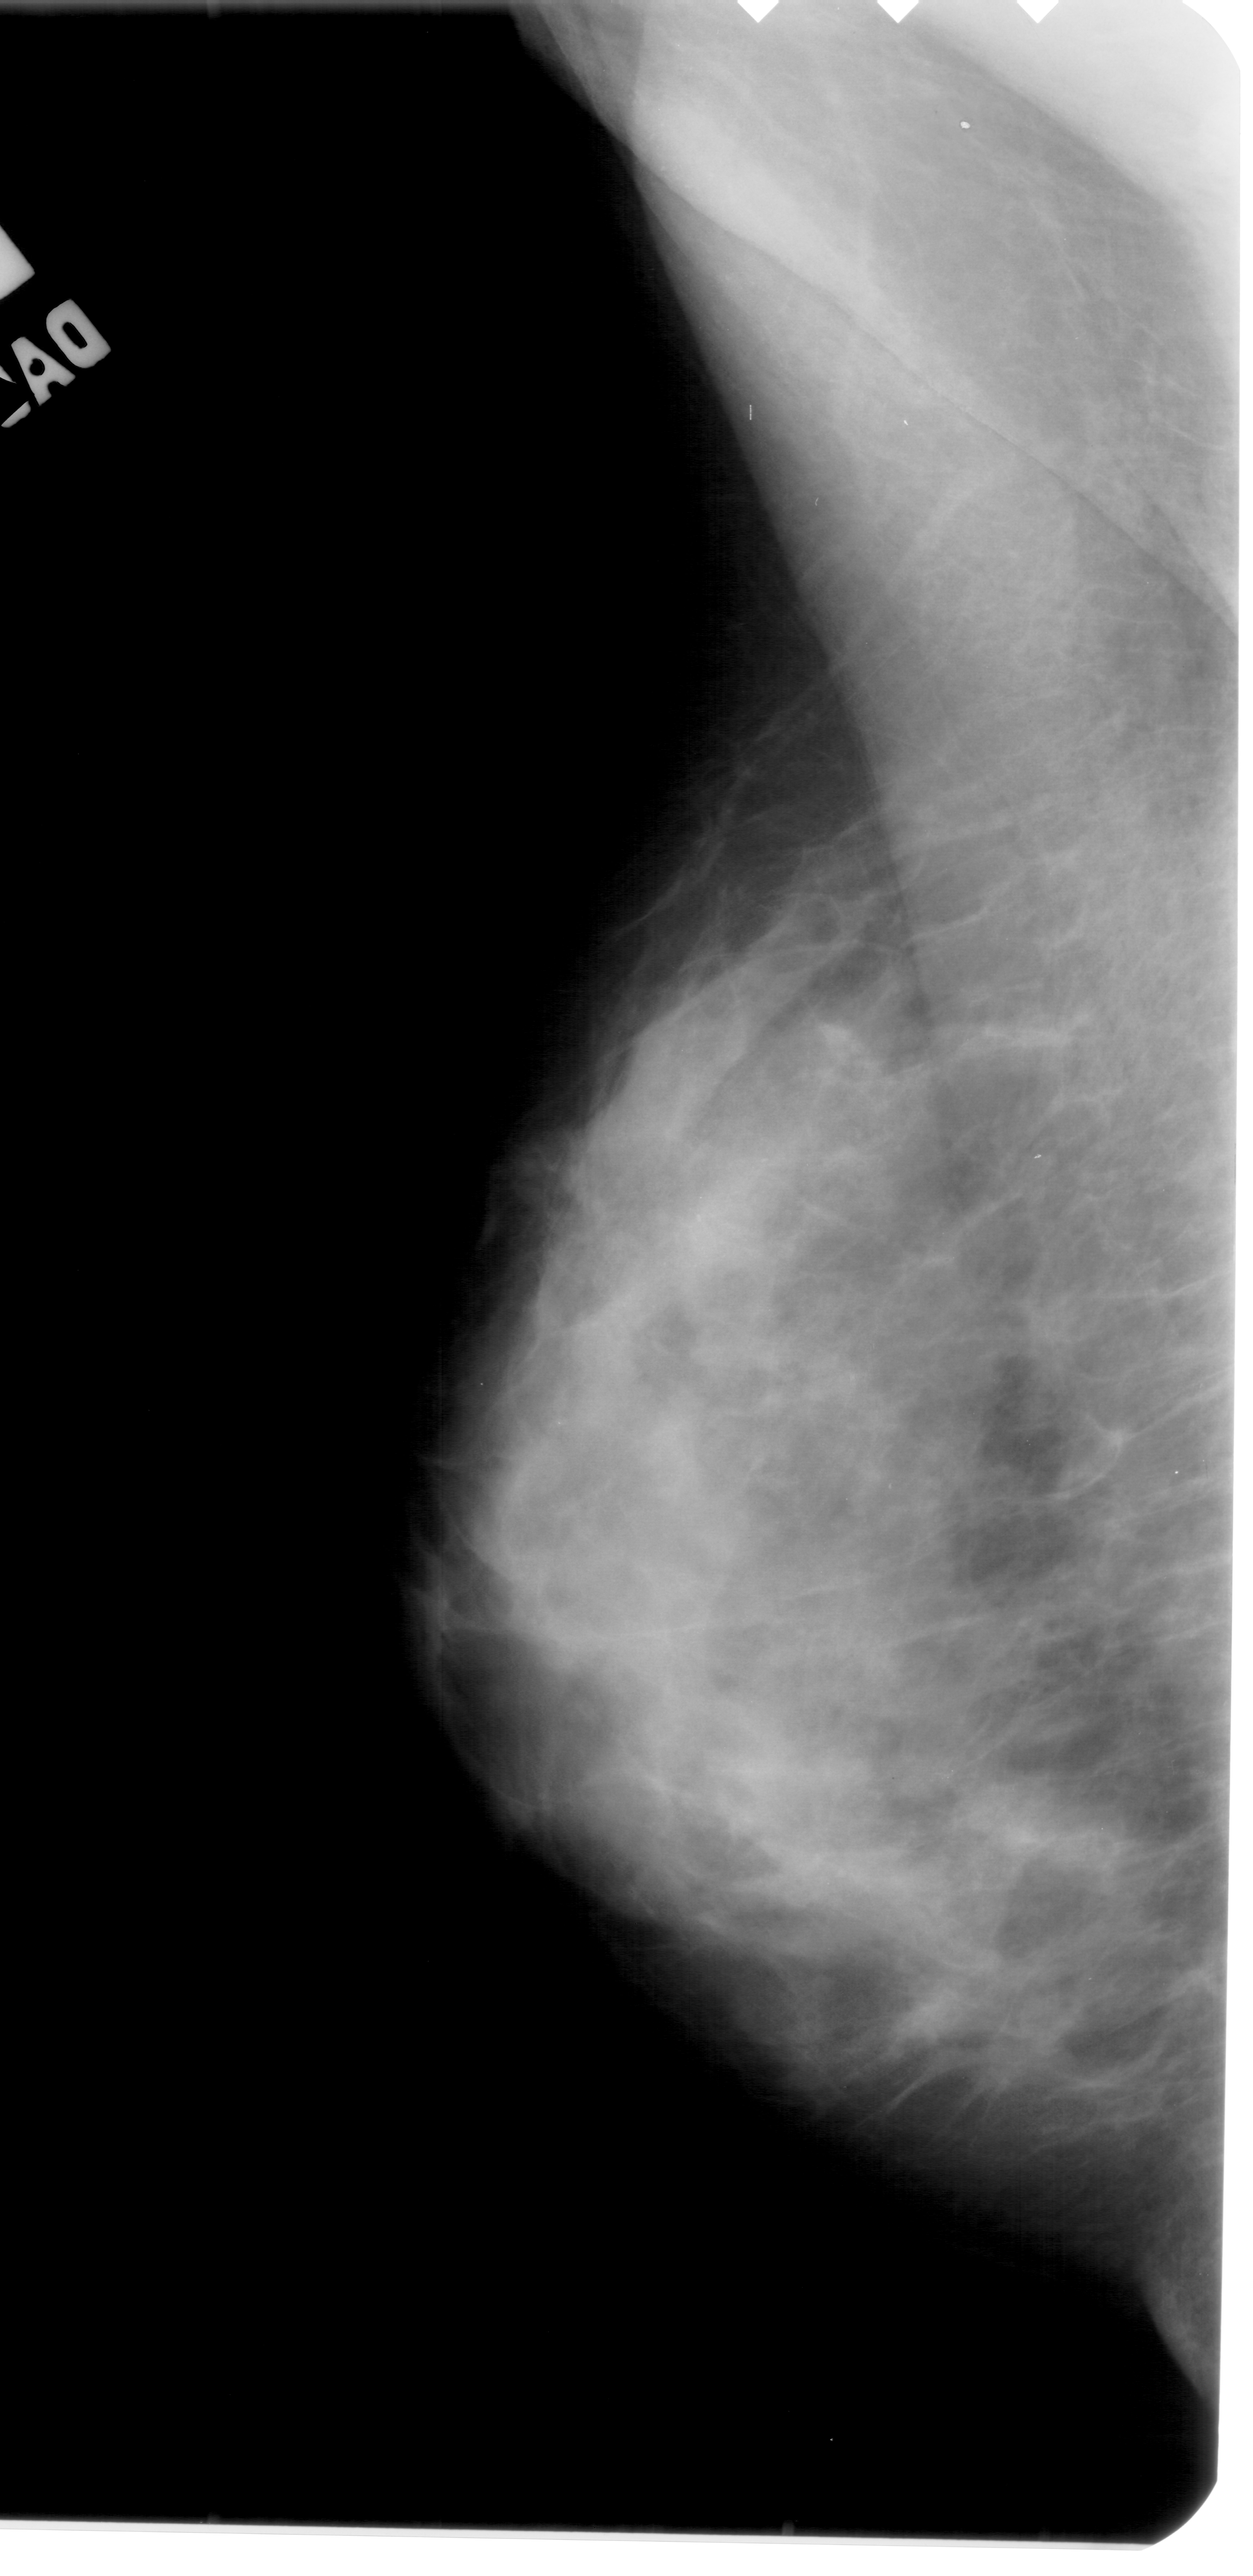
Scanned film-screen mammogram, left breast, MLO view, breast composition: extremely dense (BI-RADS density category 4 of 4).
Finding: calcifications, morphology pleomorphic, distribution segmental; BI-RADS assessment category 4; pathology (as recorded): benign.